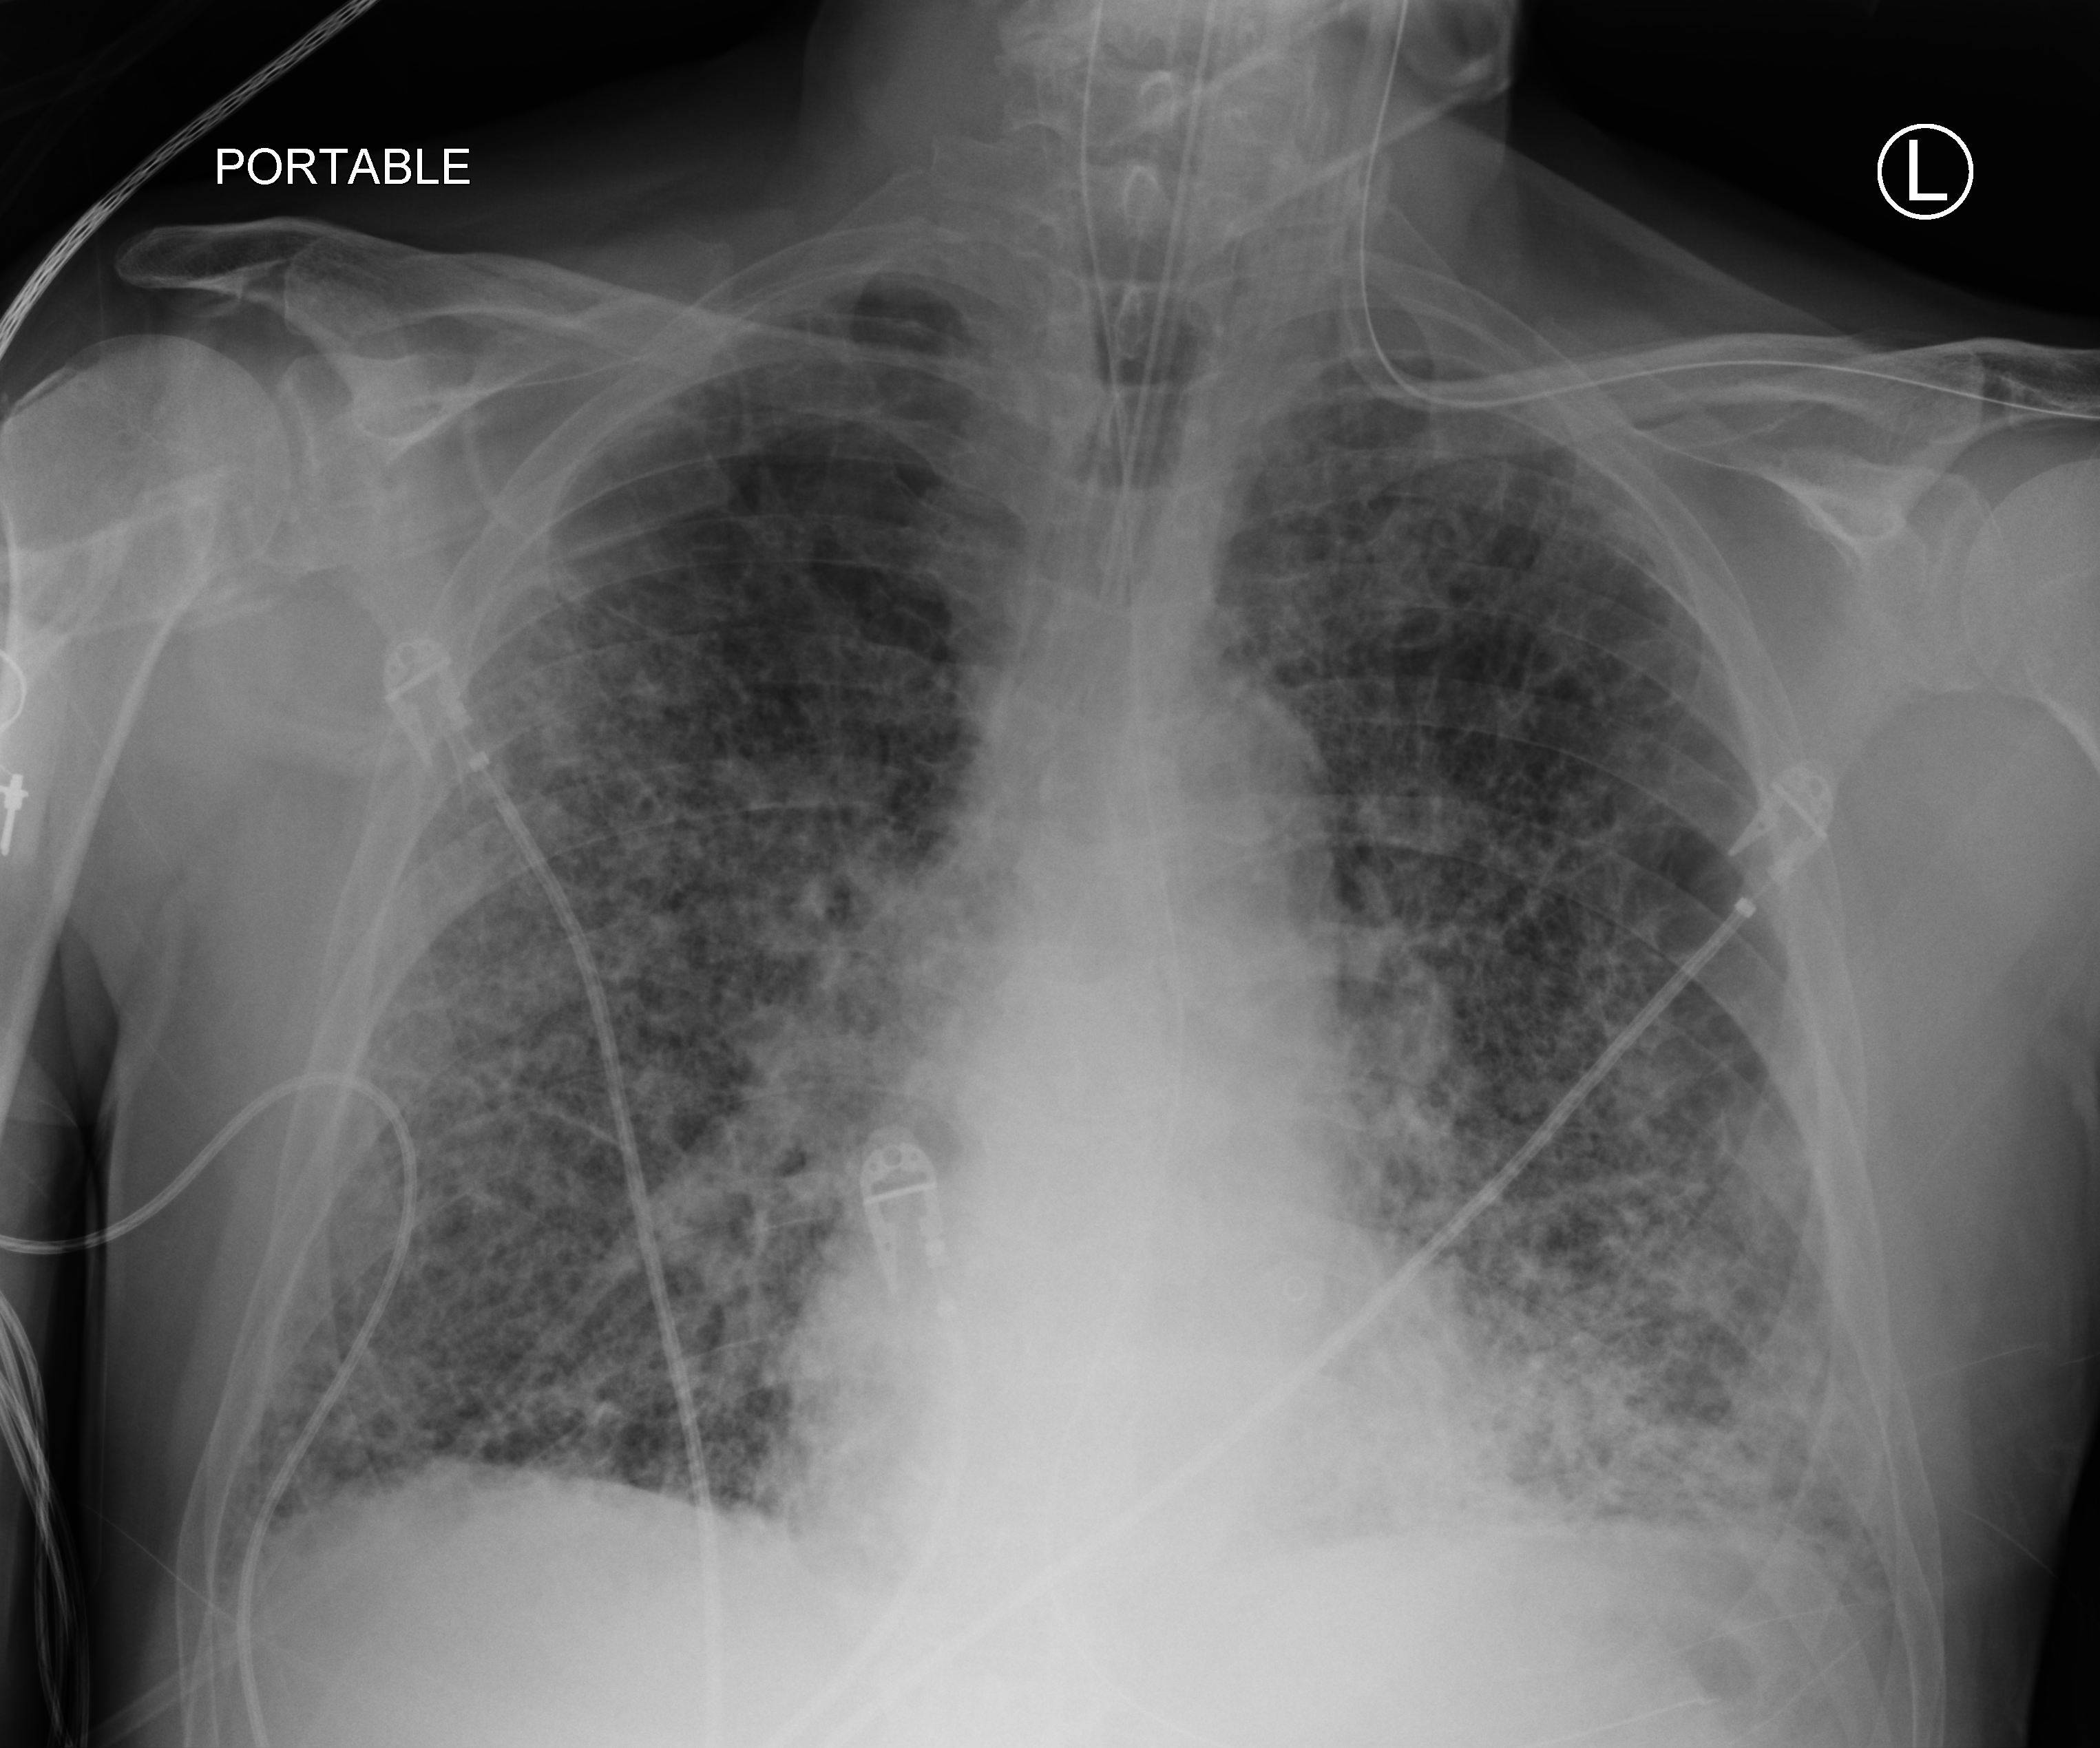
Bedside chest radiograph (computed radiography), anteroposterior (AP) projection. Patient hospitalised with COVID-19; male, aged 75–90 years.
Admission-level facts for this patient (not findings on this image; timing relative to this image not recorded):
- mechanically ventilated during this hospital stay: yes
- admitted to intensive care during this hospital stay: yes
- COPD (admission record): no